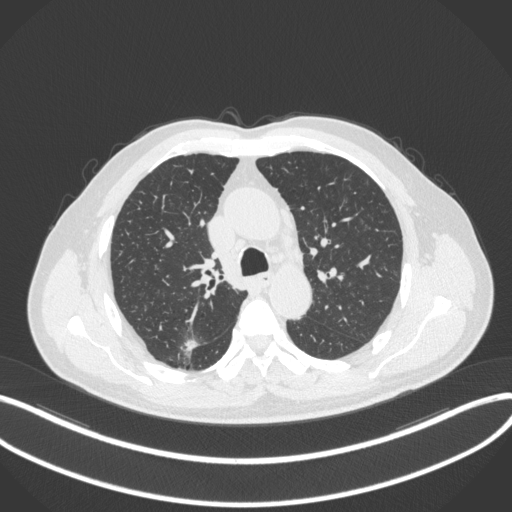
Chest CT, one axial slice. Position 253 of 366 along the scan axis. Lung window (W 1500 / L -600 HU). 1 mm slice thickness. 512 × 512 image matrix, field of view 400 × 400 mm. Patient: male, 69 years. From the clinical record (not read from this slice): clinical TNM (as recorded): T1b N0 M0; histopathological grade: G2-3.
Outlined on this slice (bounding box drawn by a radiologist):
- lung tumour (recorded histology: adenocarcinoma): bounding box <182,334,202,357> (left, top, right, bottom; pixels)